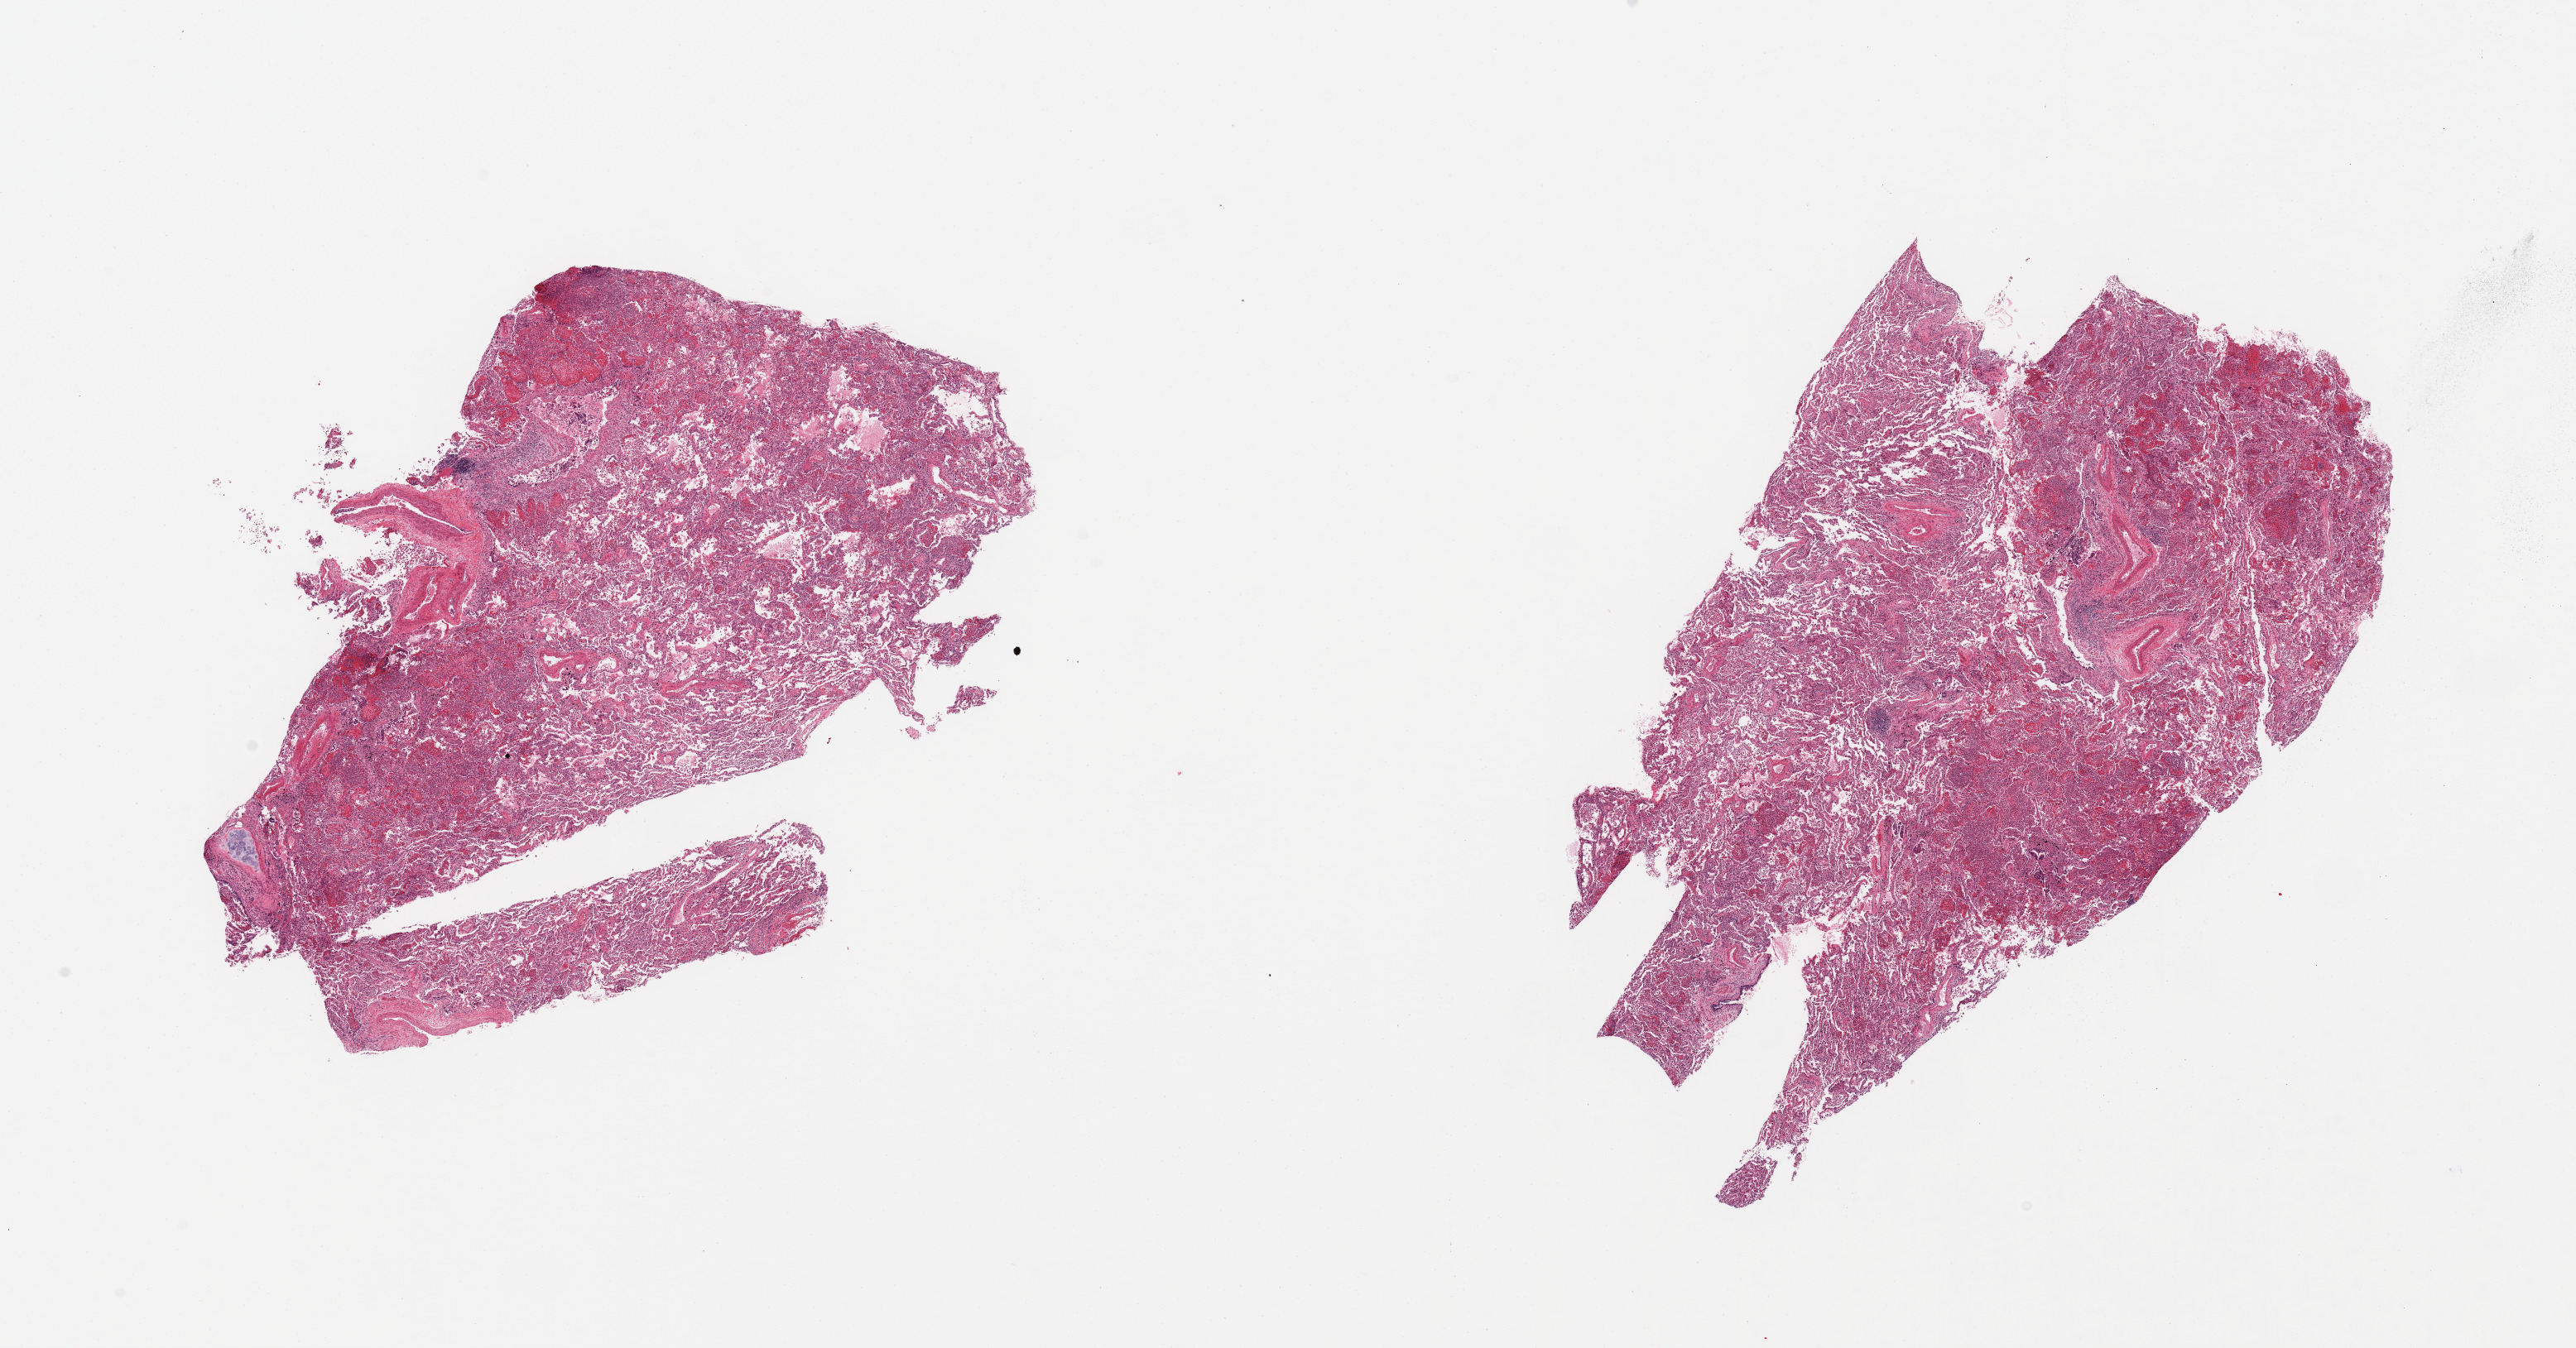
Digitized haematoxylin and eosin-stained section — shown as a low-resolution overview of the whole scanned area (about 24.6 x 12.9 mm); PAXgene-fixed, paraffin-embedded tissue; target tissue: lung; tissue donor sample.
- reviewer comment on this tissue sample: 2 pieces; extensive pneumonia